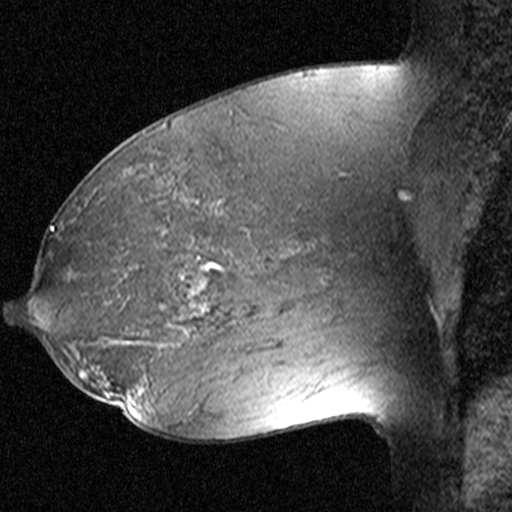
Breast MRI (dynamic contrast-enhanced), one sagittal slice; slice 26 of 44 in the series (ordered by position); dynamic contrast-enhanced study with each time point stored as its own series, time point 2 of 3 at this slice position (early post-contrast, ordered by acquisition time); 1.5 T; TE 4.5 ms, TR 11 ms; 3 mm slice thickness; 512 × 512 image matrix, field of view 200 × 200 mm. Patient: female, 38 years. From the clinical record (not read from this slice): setting: breast cancer imaged before/during neoadjuvant chemotherapy; receptor status: HR-positive, HER2-negative.
Structures marked on this image (semi-automatically segmented with operator editing):
- analysis volume of interest (the breast-tissue region the enhancement analysis was run in; not a lesion): bounding box [x1, y1, x2, y2] px = [152, 236, 253, 335]
- tumour enhancement mask (voxels above the 90 % enhancement threshold inside the analysis volume of interest): [191, 263, 223, 314]